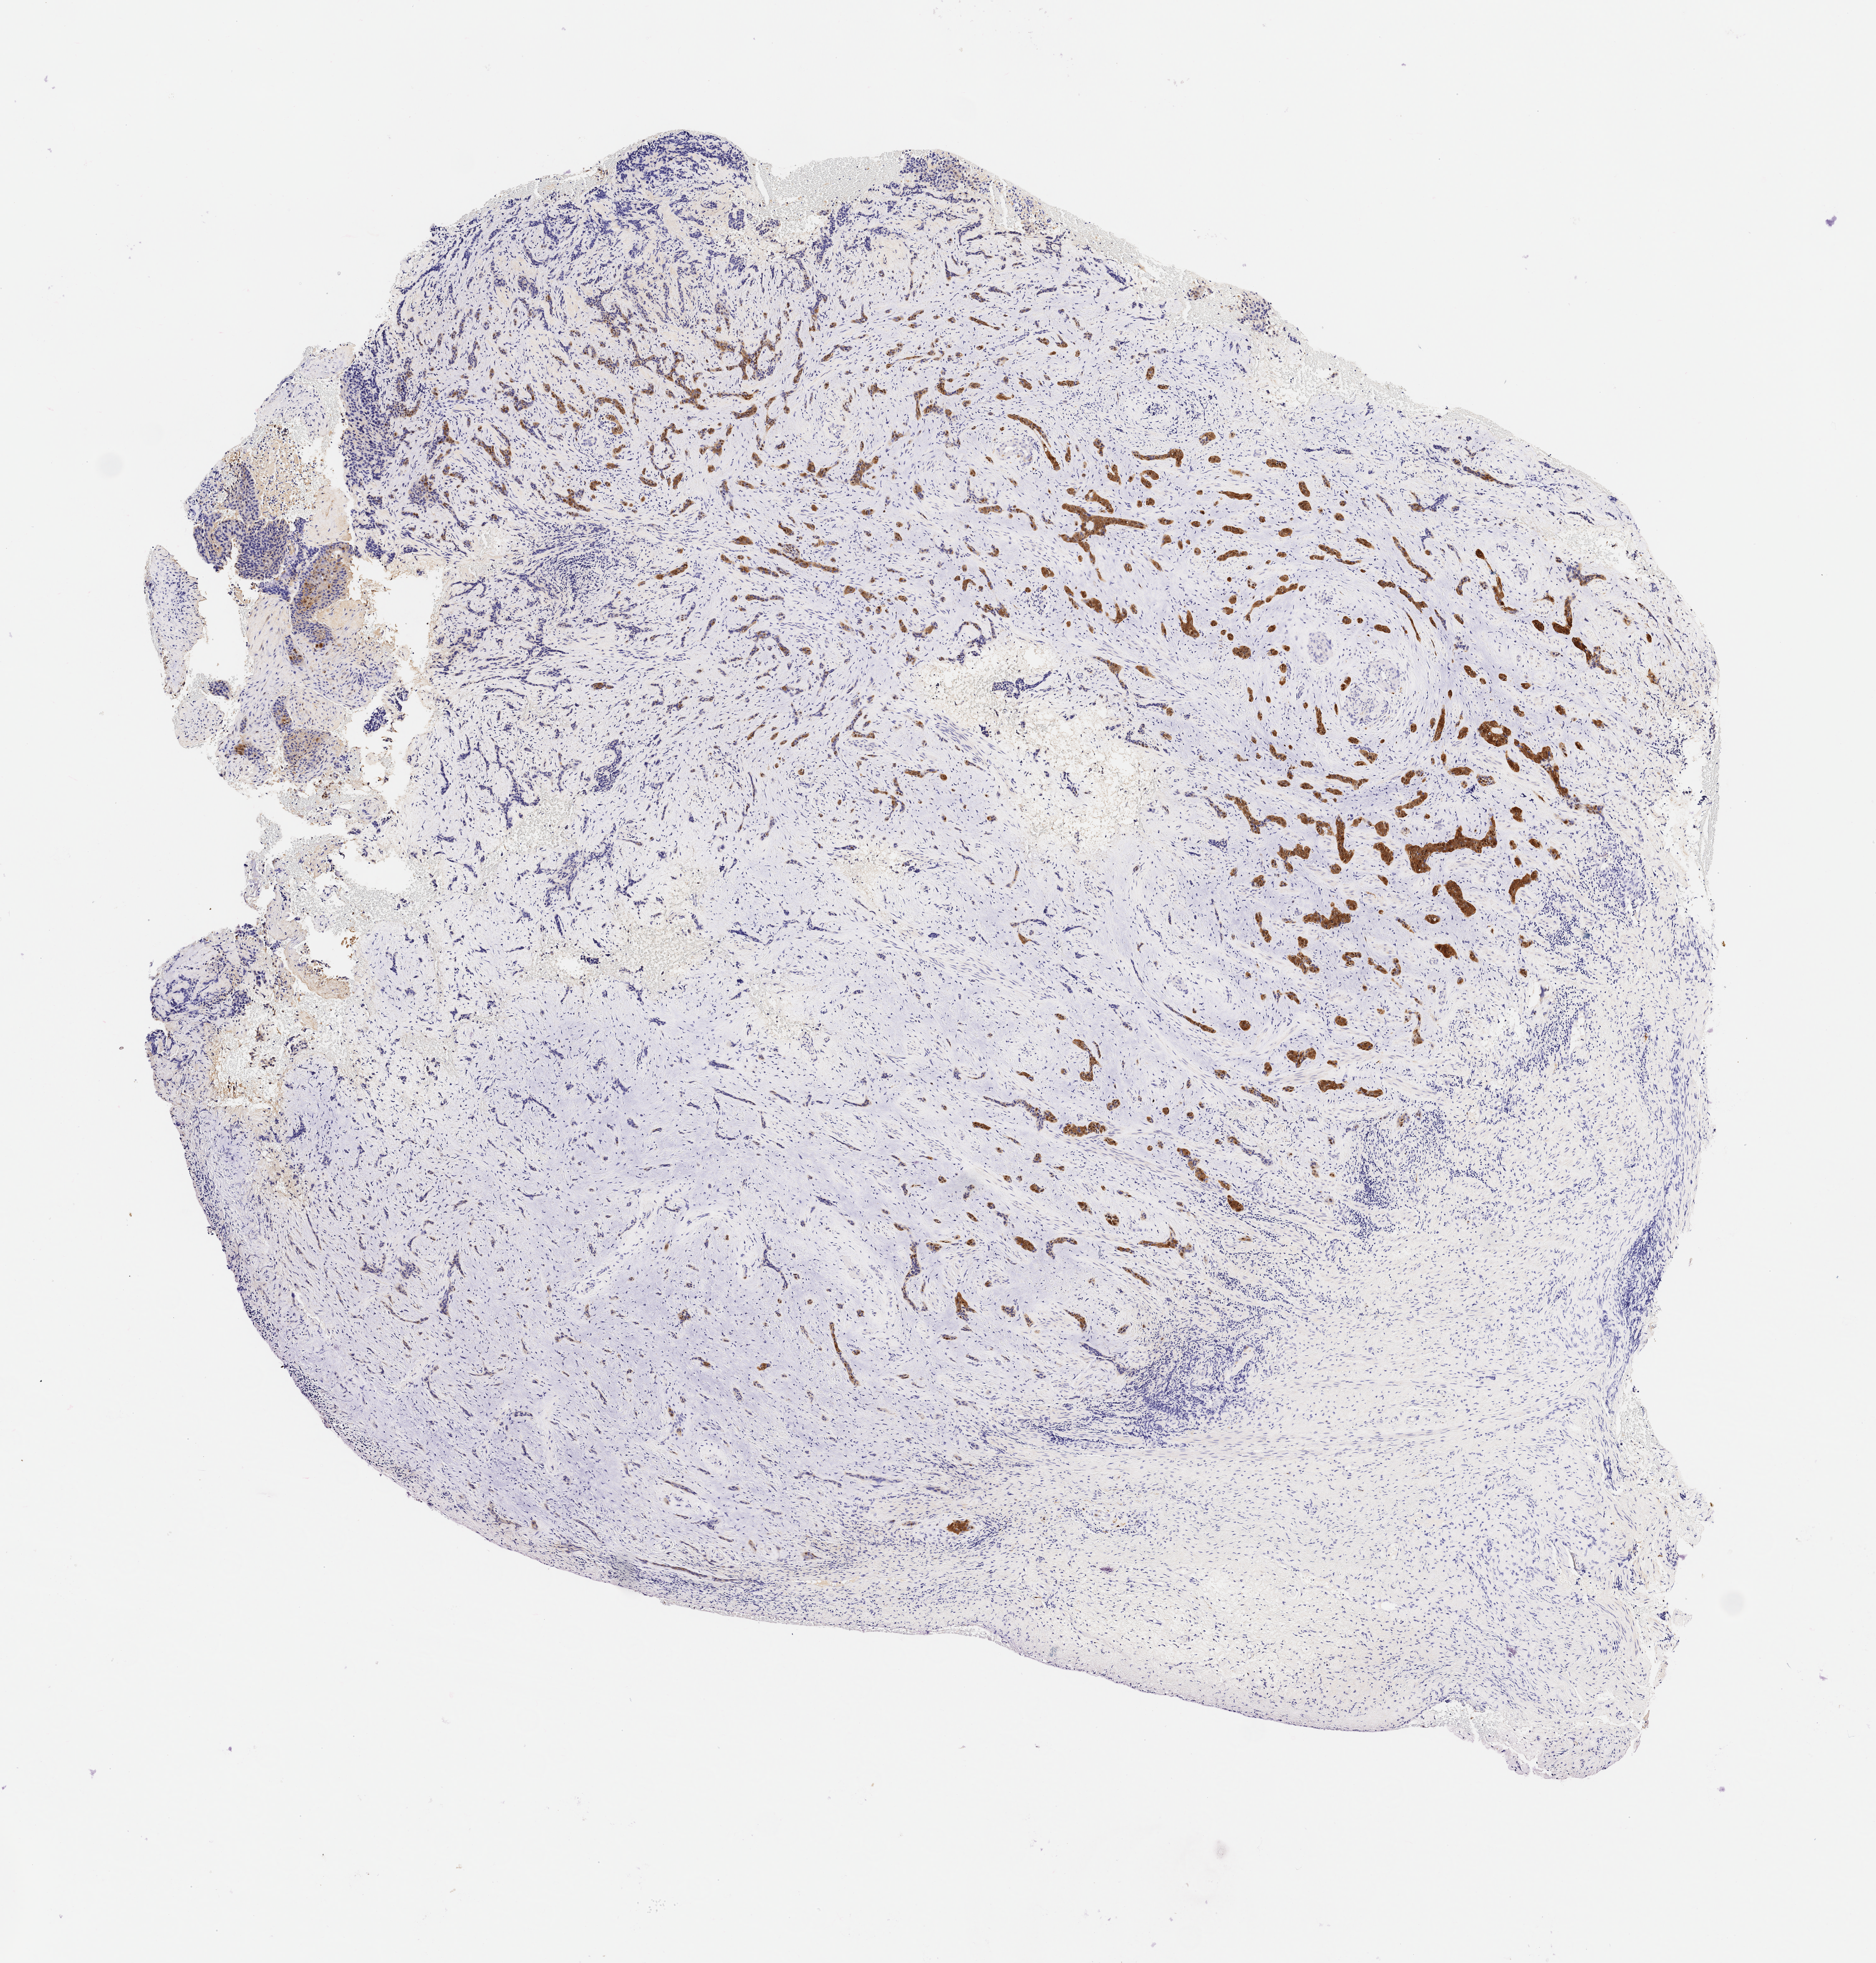
Immunohistochemistry (IHC) whole-slide image stained for p16 (p16INK4a) — whole scanned area (about 5.9 x 6.2 mm) shown as a low-resolution overview. Specimen: tumor tissue. Anatomic site: cervix. Female patient, aged 75.
Diagnosis: Squamous cell carcinoma, large cell, nonkeratinizing, NOS.